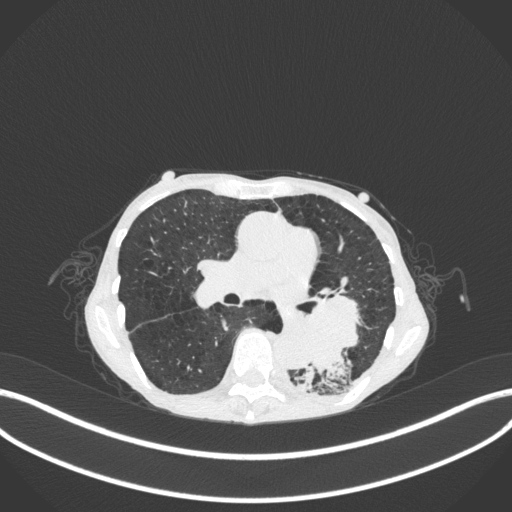
Chest CT, one axial slice. Slice 147 of 347 in the series (ordered by position). Reconstruction kernel B31f. 120 kVp. Lung window (W 1500 / L -600 HU). 1 mm slice thickness. 512 × 512 image matrix, field of view 400 × 400 mm. Female patient, age 70 years. From the clinical record (not read from this slice): clinical TNM (as recorded): T3 N0 M0; histopathological grade: G3.
Outlined on this slice (rectangle marked by the reading radiologist):
- lung tumour (recorded histology: small cell carcinoma): bounding box (x1, y1, x2, y2) in pixels: (291, 285, 363, 382)